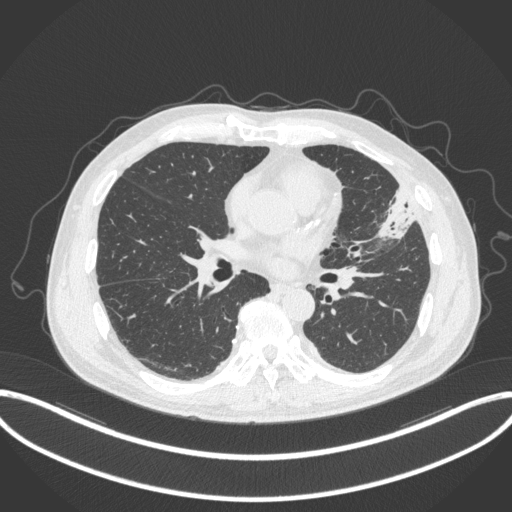
Chest CT, one axial slice; slice 162 of 382 in the series (ordered by position); reconstruction kernel B31f; 120 kVp; lung window (W 1500 / L -600 HU); 1 mm slice thickness; 512 × 512 image matrix, field of view 415 × 415 mm. Patient: male, 64 years. From the clinical record (not read from this slice): clinical TNM (as recorded): T4 N1 M0; histopathological grade: G3.
Structures marked on this image (bounding box drawn by a radiologist):
- lung tumour (recorded histology: adenocarcinoma): bounding box (x1, y1, x2, y2) in pixels: (373, 179, 416, 243)